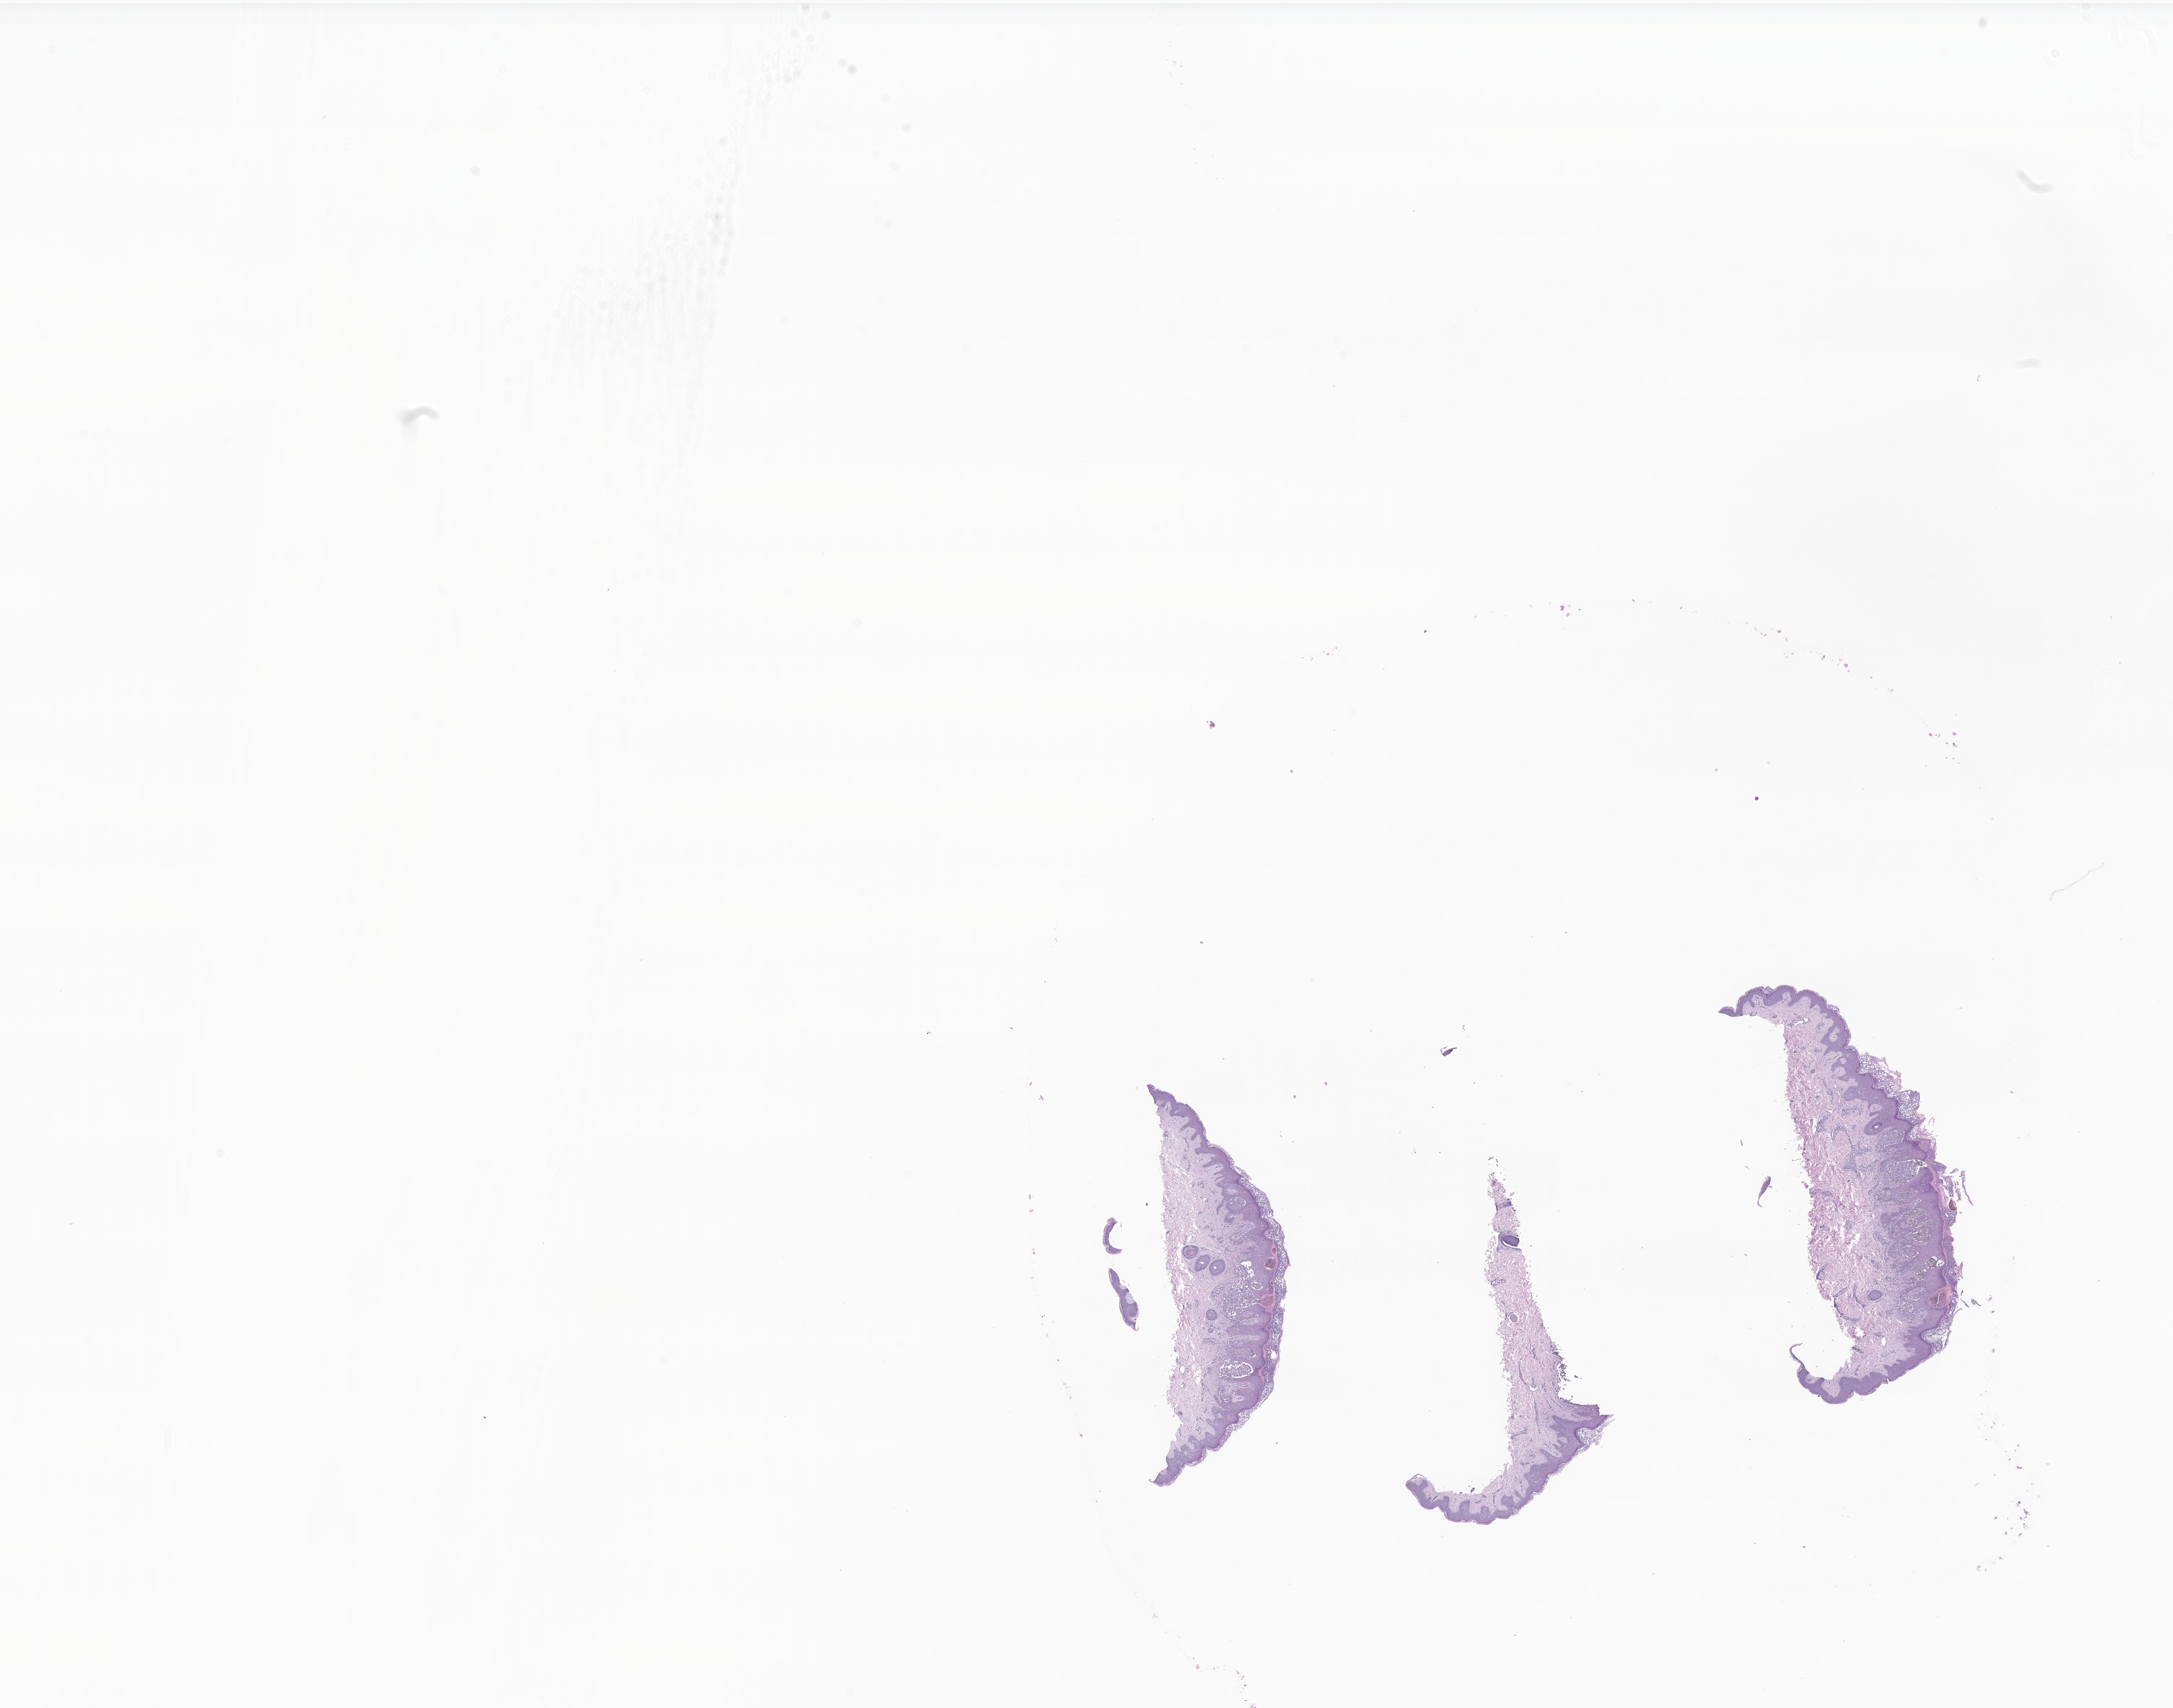
Digitized hematoxylin and eosin (H&E)-stained section of tumor tissue from the skin, a low-resolution overview of the entire scanned area, about 22.0 x 17.3 mm; formalin-fixed paraffin-embedded section. Patient female; age 102 months (8 years 6 months).
Diagnosis (ICD-O-3 morphology term): Malignant melanoma, NOS.